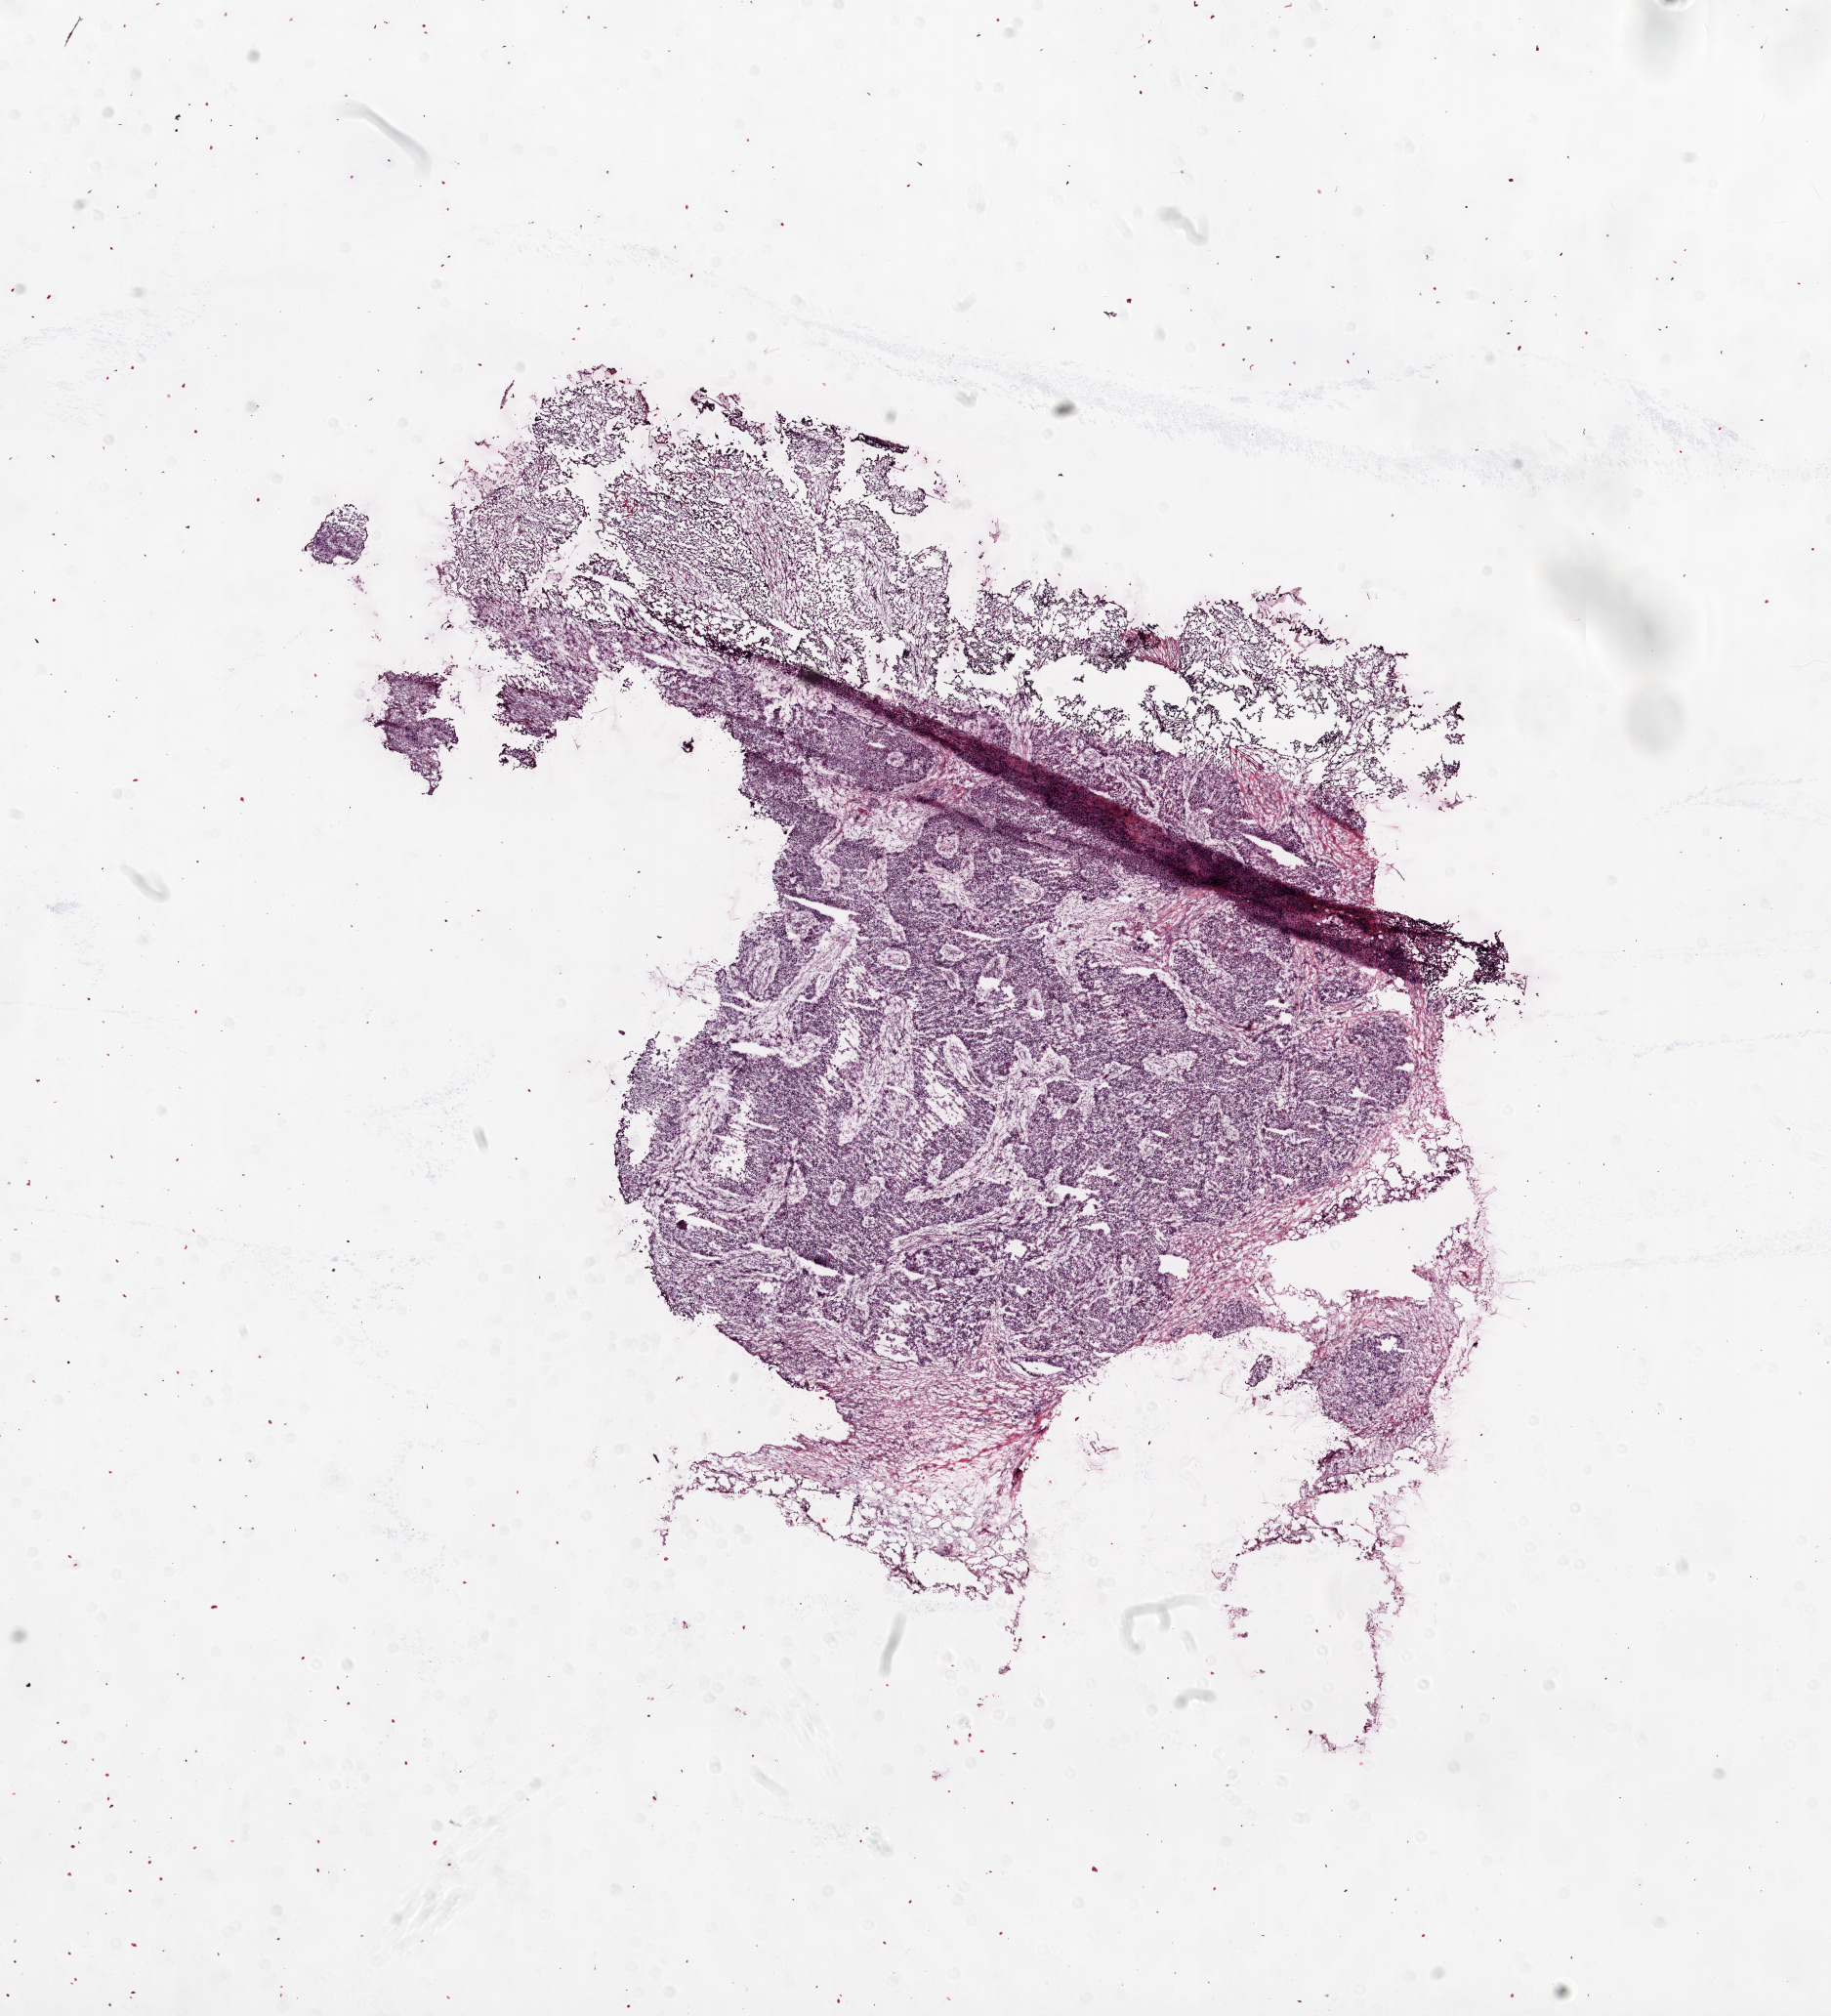
Hematoxylin and eosin (H&E) stained whole-slide image, shown as a low-resolution overview of the whole scanned area (about 15.0 x 16.6 mm, slide scanned at 20x); frozen section from the top of the tissue portion; primary tumour sample from the ovary. Patient: female, age at initial diagnosis 54 years. Histologic grade: G2 (moderately differentiated). Slide review estimates, as recorded: tumour cells 80%, tumour nuclei 90%, normal cells 0%, stromal cells 20%, necrosis 0%.
• FIGO stage: IIIC
• diagnosis: Serous cystadenocarcinoma, NOS